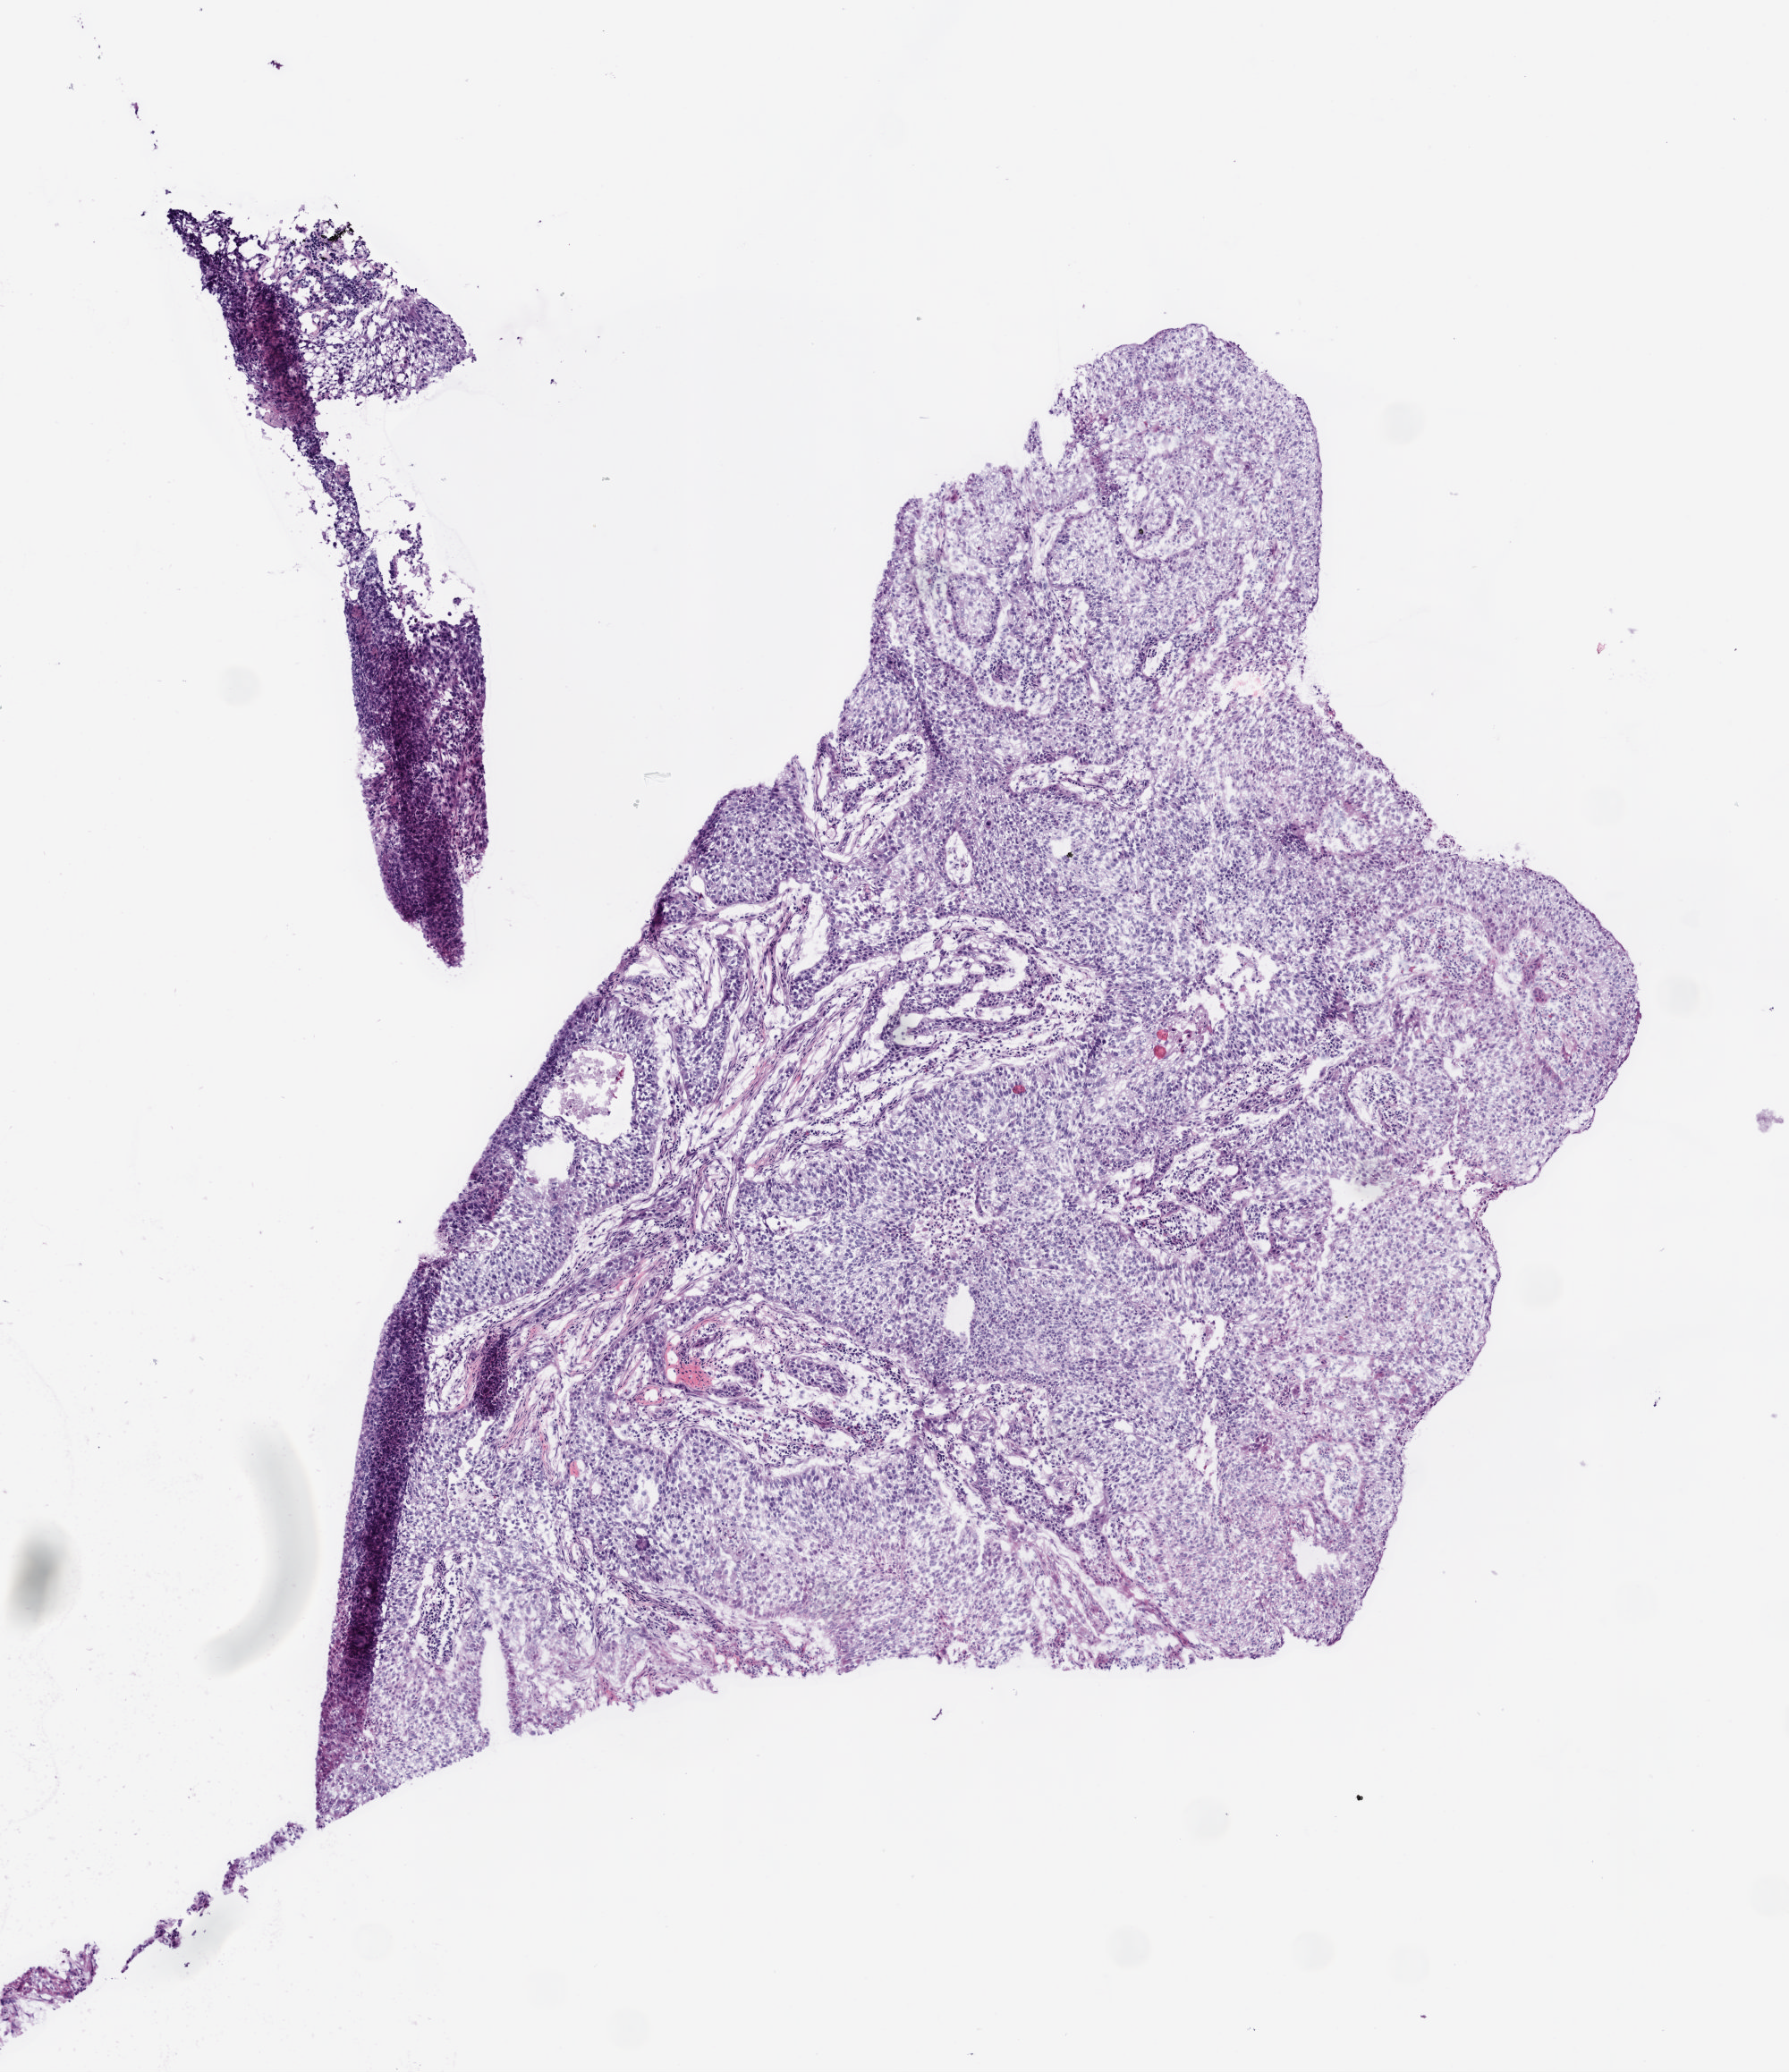
H&E-stained whole-slide image, shown as a low-resolution overview of the whole scanned area (about 4.0 x 4.6 mm). Frozen section from the bottom of the tissue portion. Lung, primary tumour sample. Male, age 73 years at initial diagnosis. Pathologist review of this section (percent, as recorded): tumour cells 90%, tumour nuclei 90%, normal cells 0%, stromal cells 8%, necrosis 2%. Inflammatory infiltration, as recorded: lymphocyte infiltration 3%.
AJCC pathologic stage: IV. Diagnosis: Squamous cell carcinoma, NOS (lower lobe, lung).